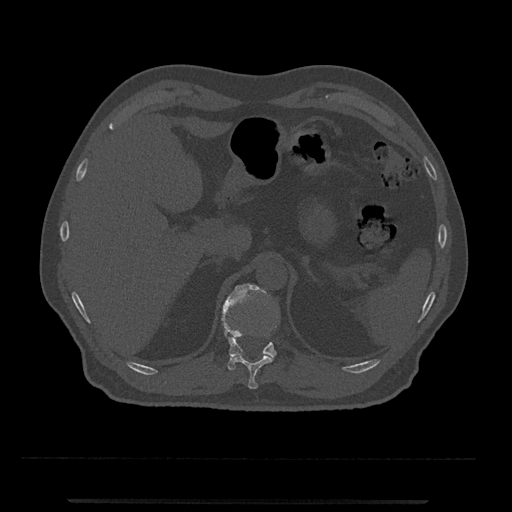
CT including the spine, one axial slice; position 434 of 797 along the scan axis; reconstruction kernel Br40s/3; bone window (W 1800 / L 400 HU); 0.5 mm slice thickness; 512 × 512 image matrix, field of view 419 × 419 mm. Male patient, age 63 years. Case-level facts recorded for this patient, not image findings: primary cancer: prostate.
Structures marked on this image (semi-automatic segmentation, software-assisted and operator-edited):
- T11 vertebra: box from (x=233, y=327) to (x=276, y=389) px
- T12 vertebra: (x=222, y=283)–(x=277, y=371)